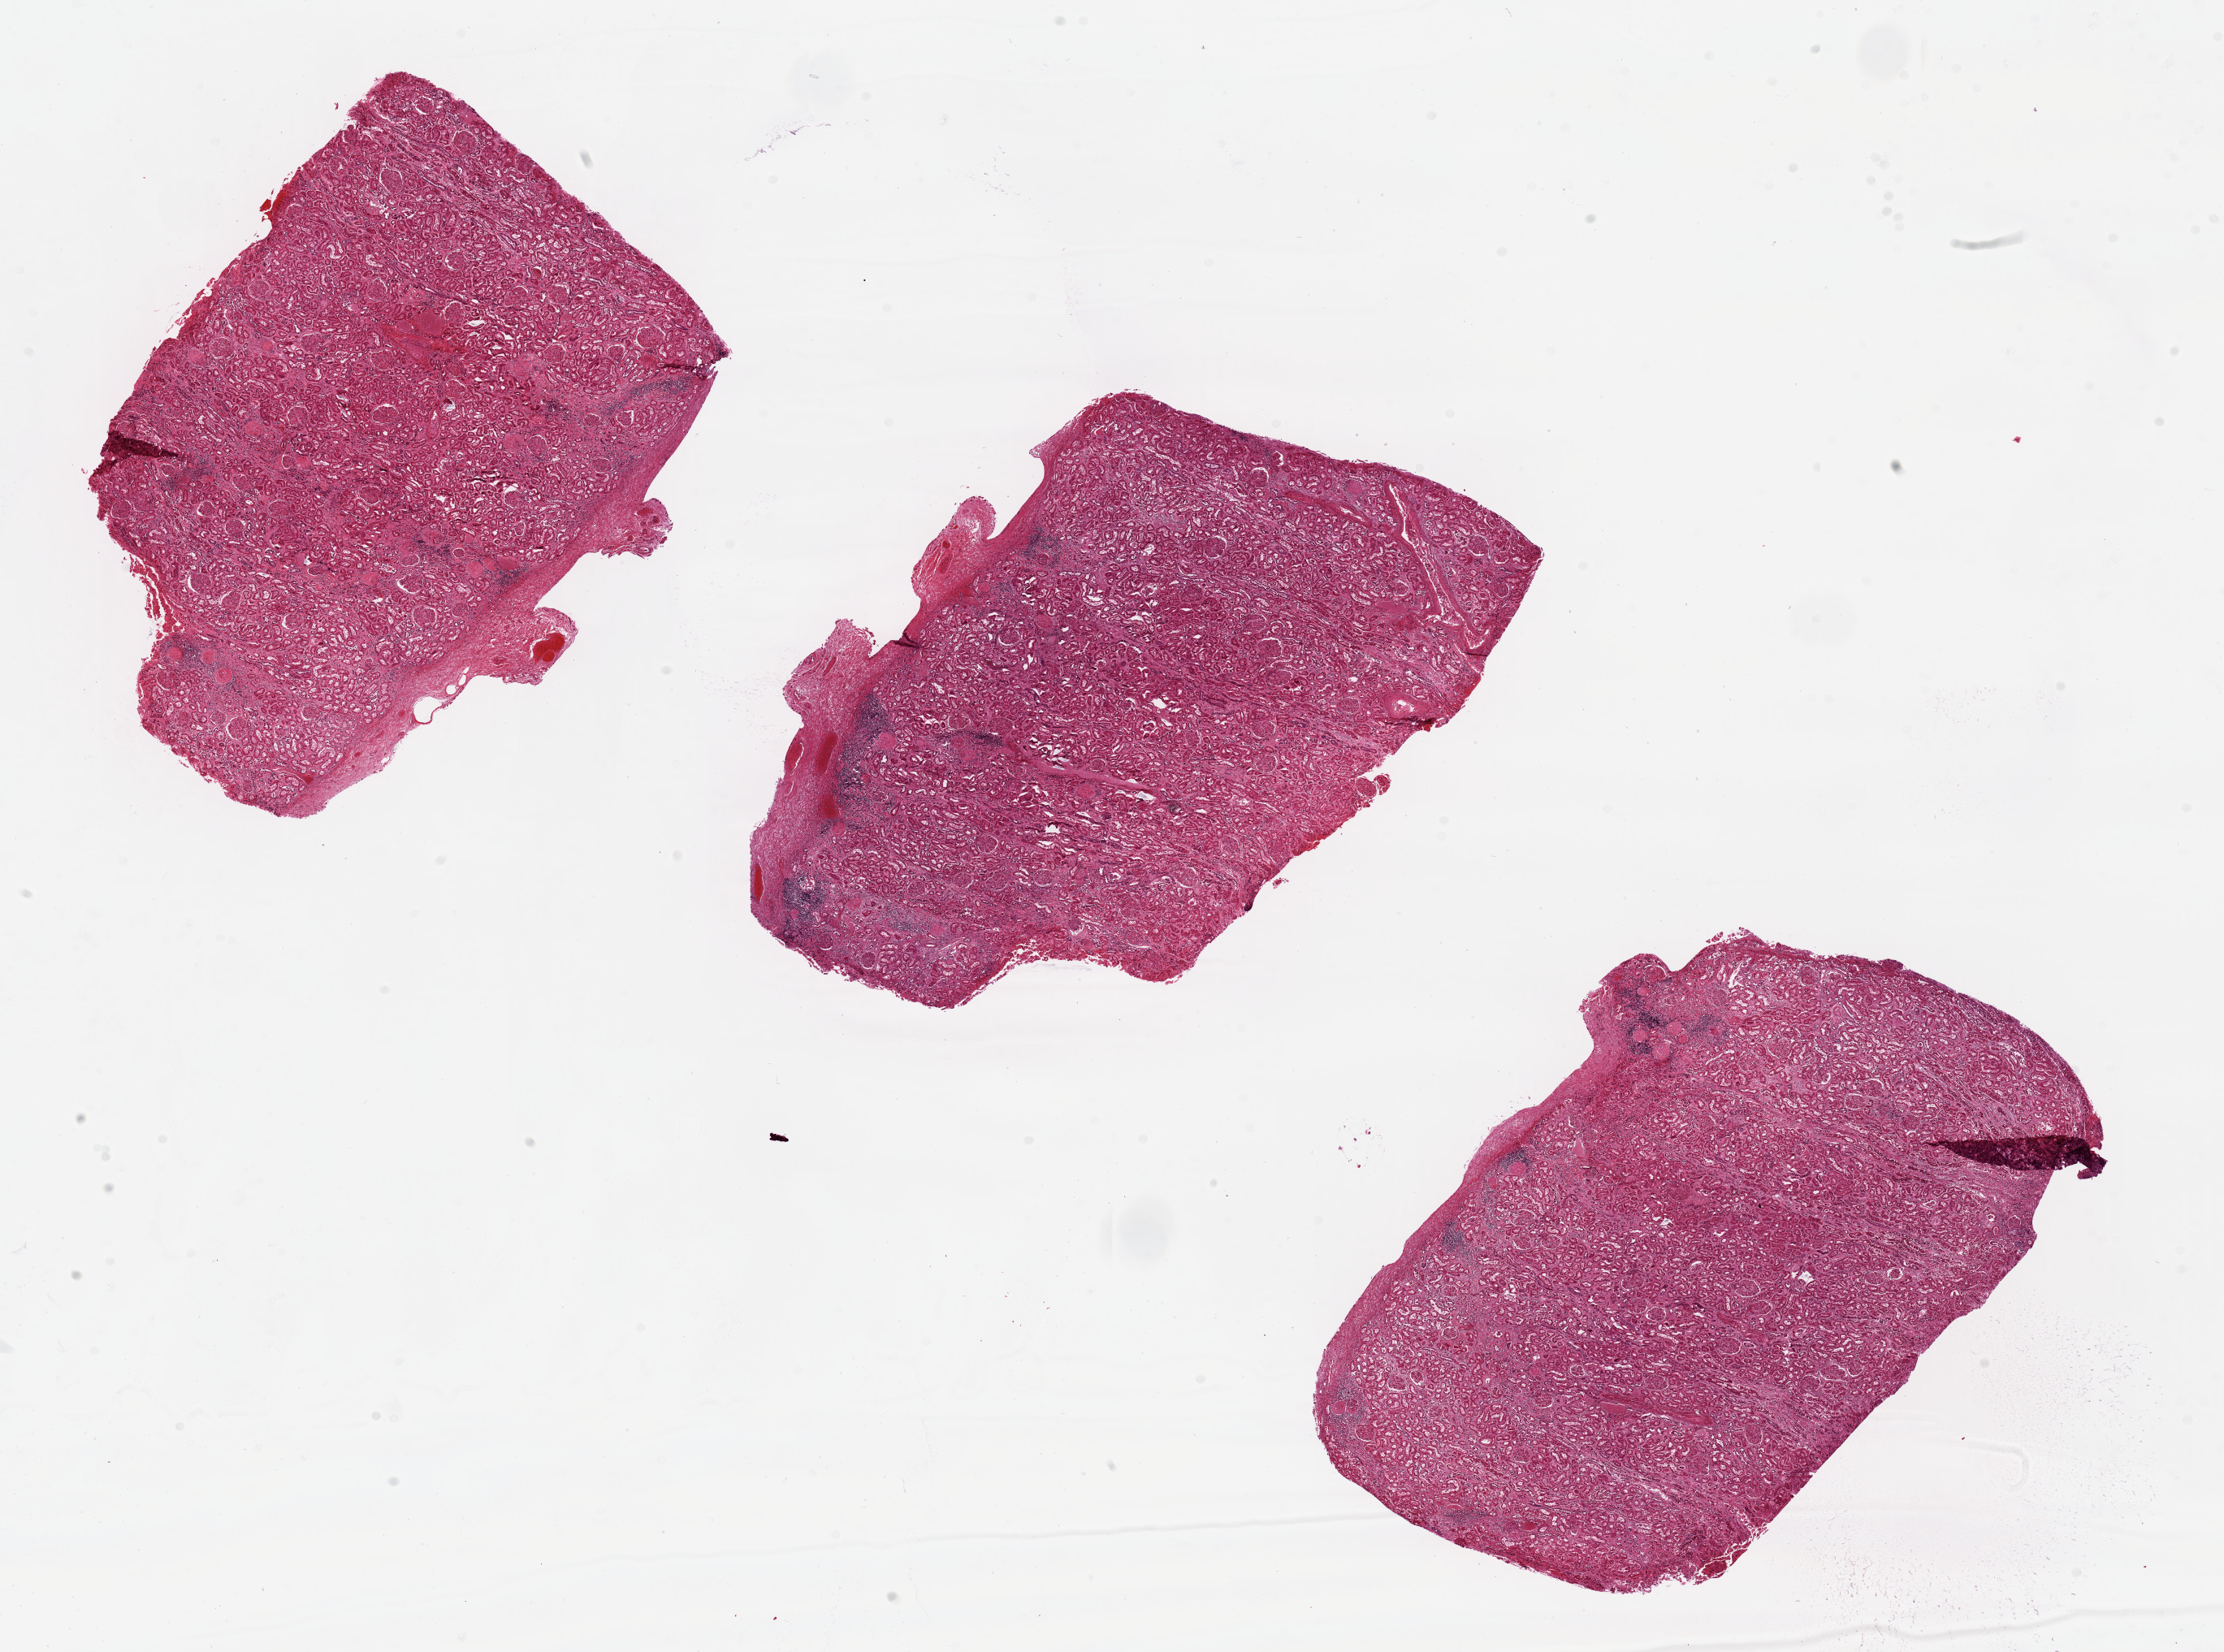
Hematoxylin and eosin (H&E) whole-slide image, a low-resolution overview of the entire scanned area, about 21.7 x 16.1 mm; PAXgene-fixed, paraffin-embedded tissue; section of renal cortex (target tissue); donor tissue sample.
Pathologist's review note for this sample: Arterio-nephrosclerosis, moderate-marked, interstitial nephritis, chronic, with interstitial fibrosis.